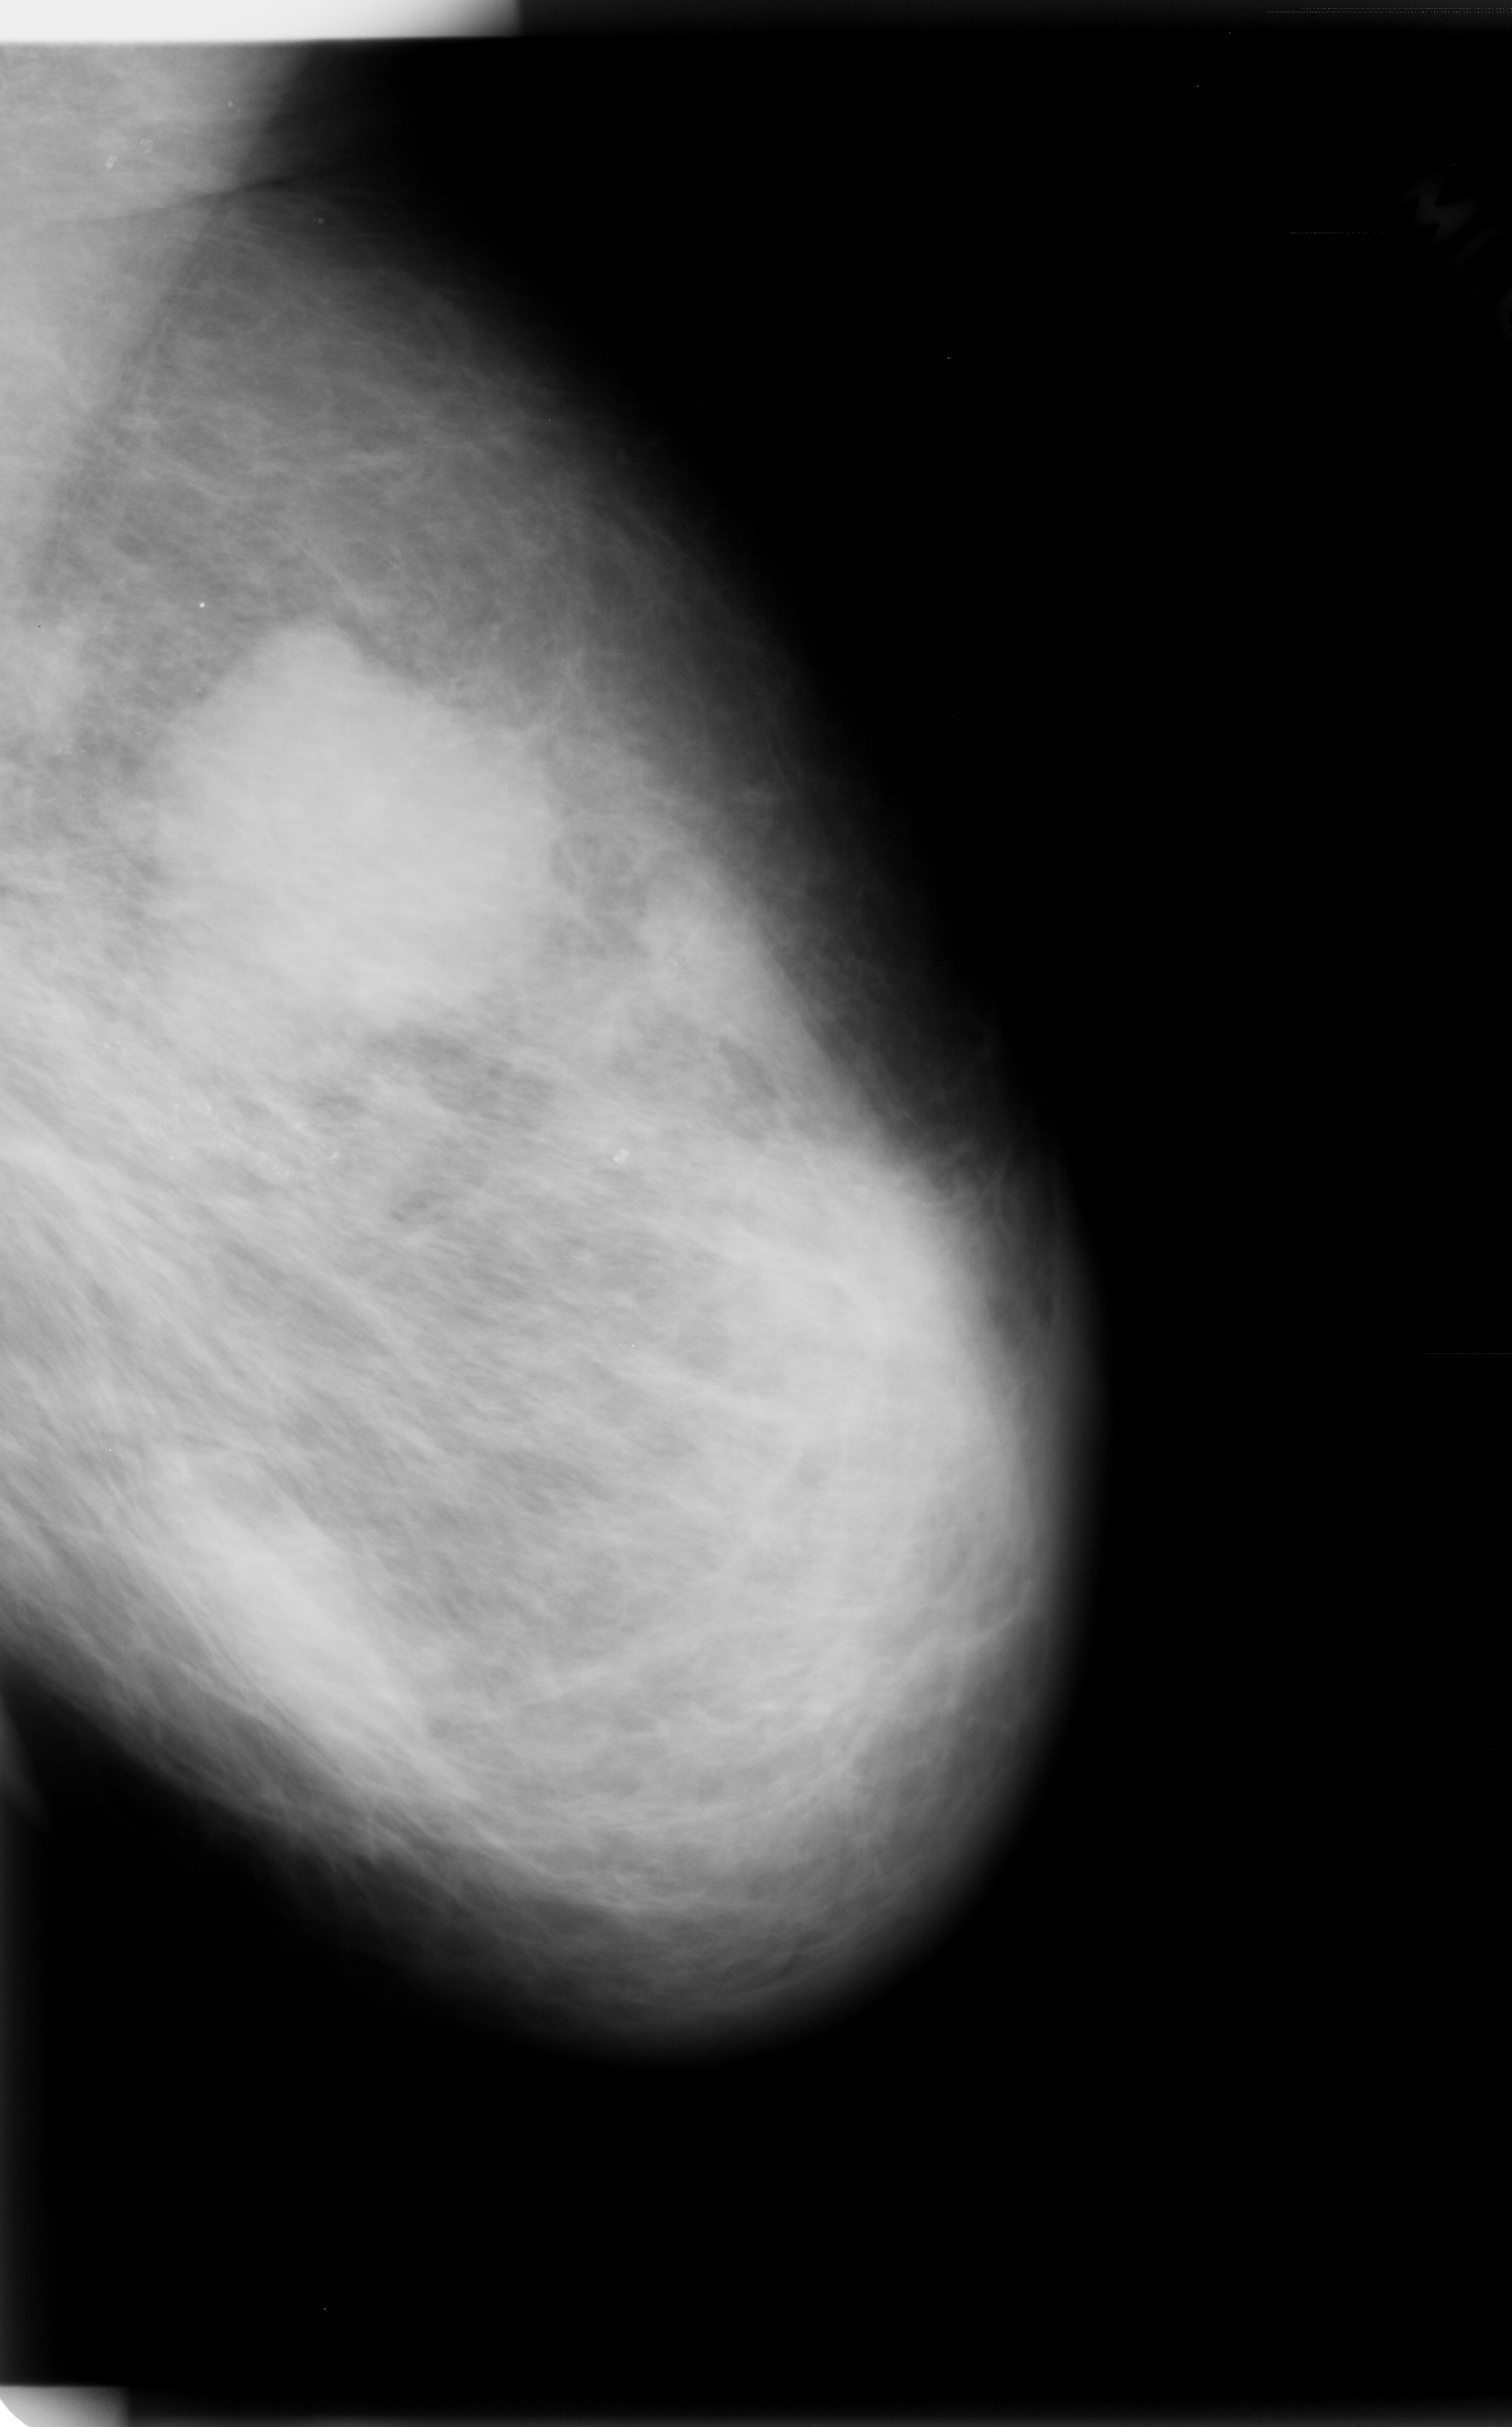
Scanned film-screen mammogram; left breast; MLO view; BI-RADS breast density category 2 (scale 1–4); 1512 × 2427 image matrix.
Expert-marked regions of interest on this image (one box per marked abnormality):
- calcifications, morphology pleomorphic, distribution segmental; BI-RADS assessment category 5; subtlety rating 5 on a 1 (subtle) to 5 (obvious) scale; pathology result (as recorded, not read from the image): malignant: bounding box <3,552,1128,2095> (left, top, right, bottom; pixels)